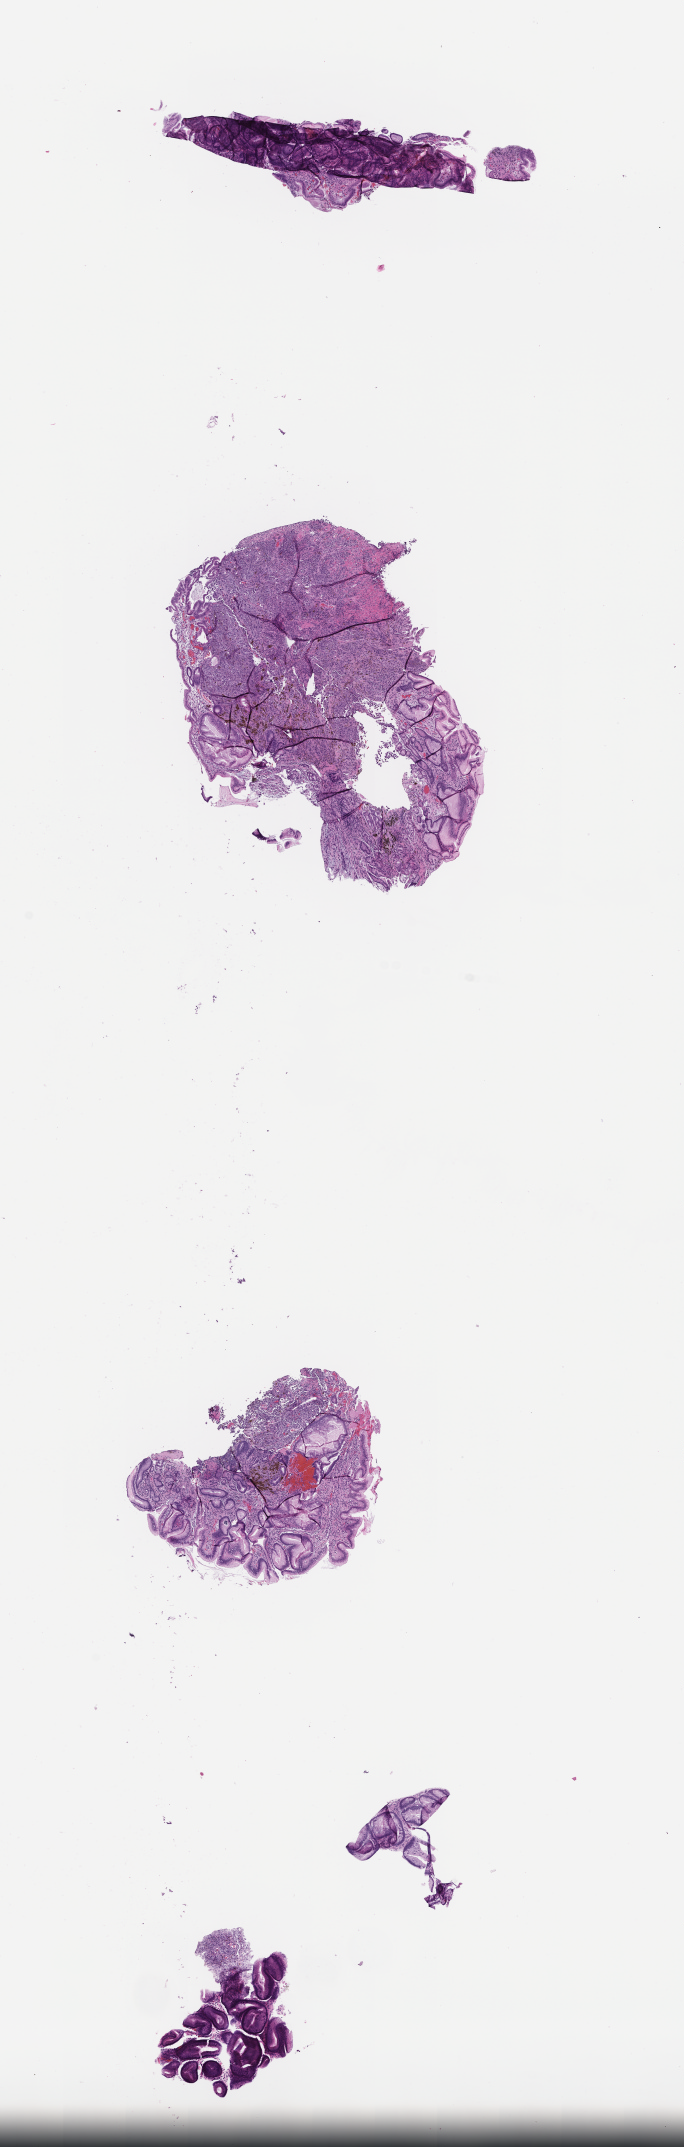
Whole-slide image, hematoxylin and eosin (H&E) stain, shown as a low-resolution overview of the whole scanned area (about 5.5 x 17.4 mm). Formalin-fixed, paraffin-embedded (FFPE) tissue. Patient: male.
* this section: metastasis (sampled organ not recorded)
* patient diagnosis (primary): Melanoma